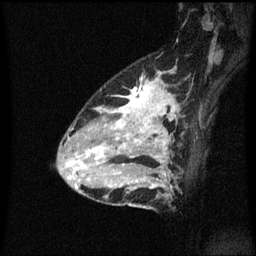
Breast MRI (dynamic contrast-enhanced), one sagittal slice. Slice 41 of 60 in the series (ordered by position). Dynamic contrast-enhanced series, image 2 of 3 at this slice position (ordered by acquisition). 1.5 T. TE 4.2 ms, TR 8.4 ms. 2 mm slice thickness. 256 × 256 image matrix, field of view 200 × 200 mm. Patient: female, 34 years. From the clinical record (not read from this slice): setting: breast cancer imaged before/during neoadjuvant chemotherapy; receptor status: HR-positive, HER2-negative.
Structures marked on this image (semi-automatic segmentation, software-assisted and operator-edited):
- analysis volume of interest (the breast-tissue region the enhancement analysis was run in; not a lesion): bounding box [x1, y1, x2, y2] px = [69, 72, 179, 209]
- tumour enhancement mask (voxels above the 70 % enhancement threshold inside the analysis volume of interest): [70, 80, 174, 189]